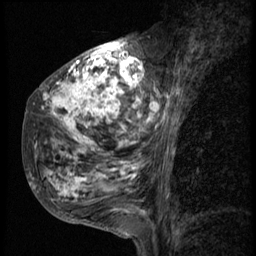
Breast MRI (dynamic contrast-enhanced), one sagittal slice. Slice 21 of 58 in the series (ordered by position). 3 images stored at this slice position (order not interpretable as contrast timing). 1.5 T. TE 4.2 ms, TR 9 ms. 2.5 mm slice thickness. 256 × 256 image matrix, field of view 180 × 180 mm. Female patient, age 50 years. Case-level facts recorded for this patient, not image findings: setting: breast cancer imaged before/during neoadjuvant chemotherapy; receptor status: triple-negative.
Structures marked on this image (semi-automatic segmentation, software-assisted and operator-edited):
- analysis volume of interest (the breast-tissue region the enhancement analysis was run in; not a lesion): bounding box (x1, y1, x2, y2) in pixels: (24, 48, 180, 214)
- tumour enhancement mask (voxels above the 140 % enhancement threshold inside the analysis volume of interest): (31, 48, 179, 209)